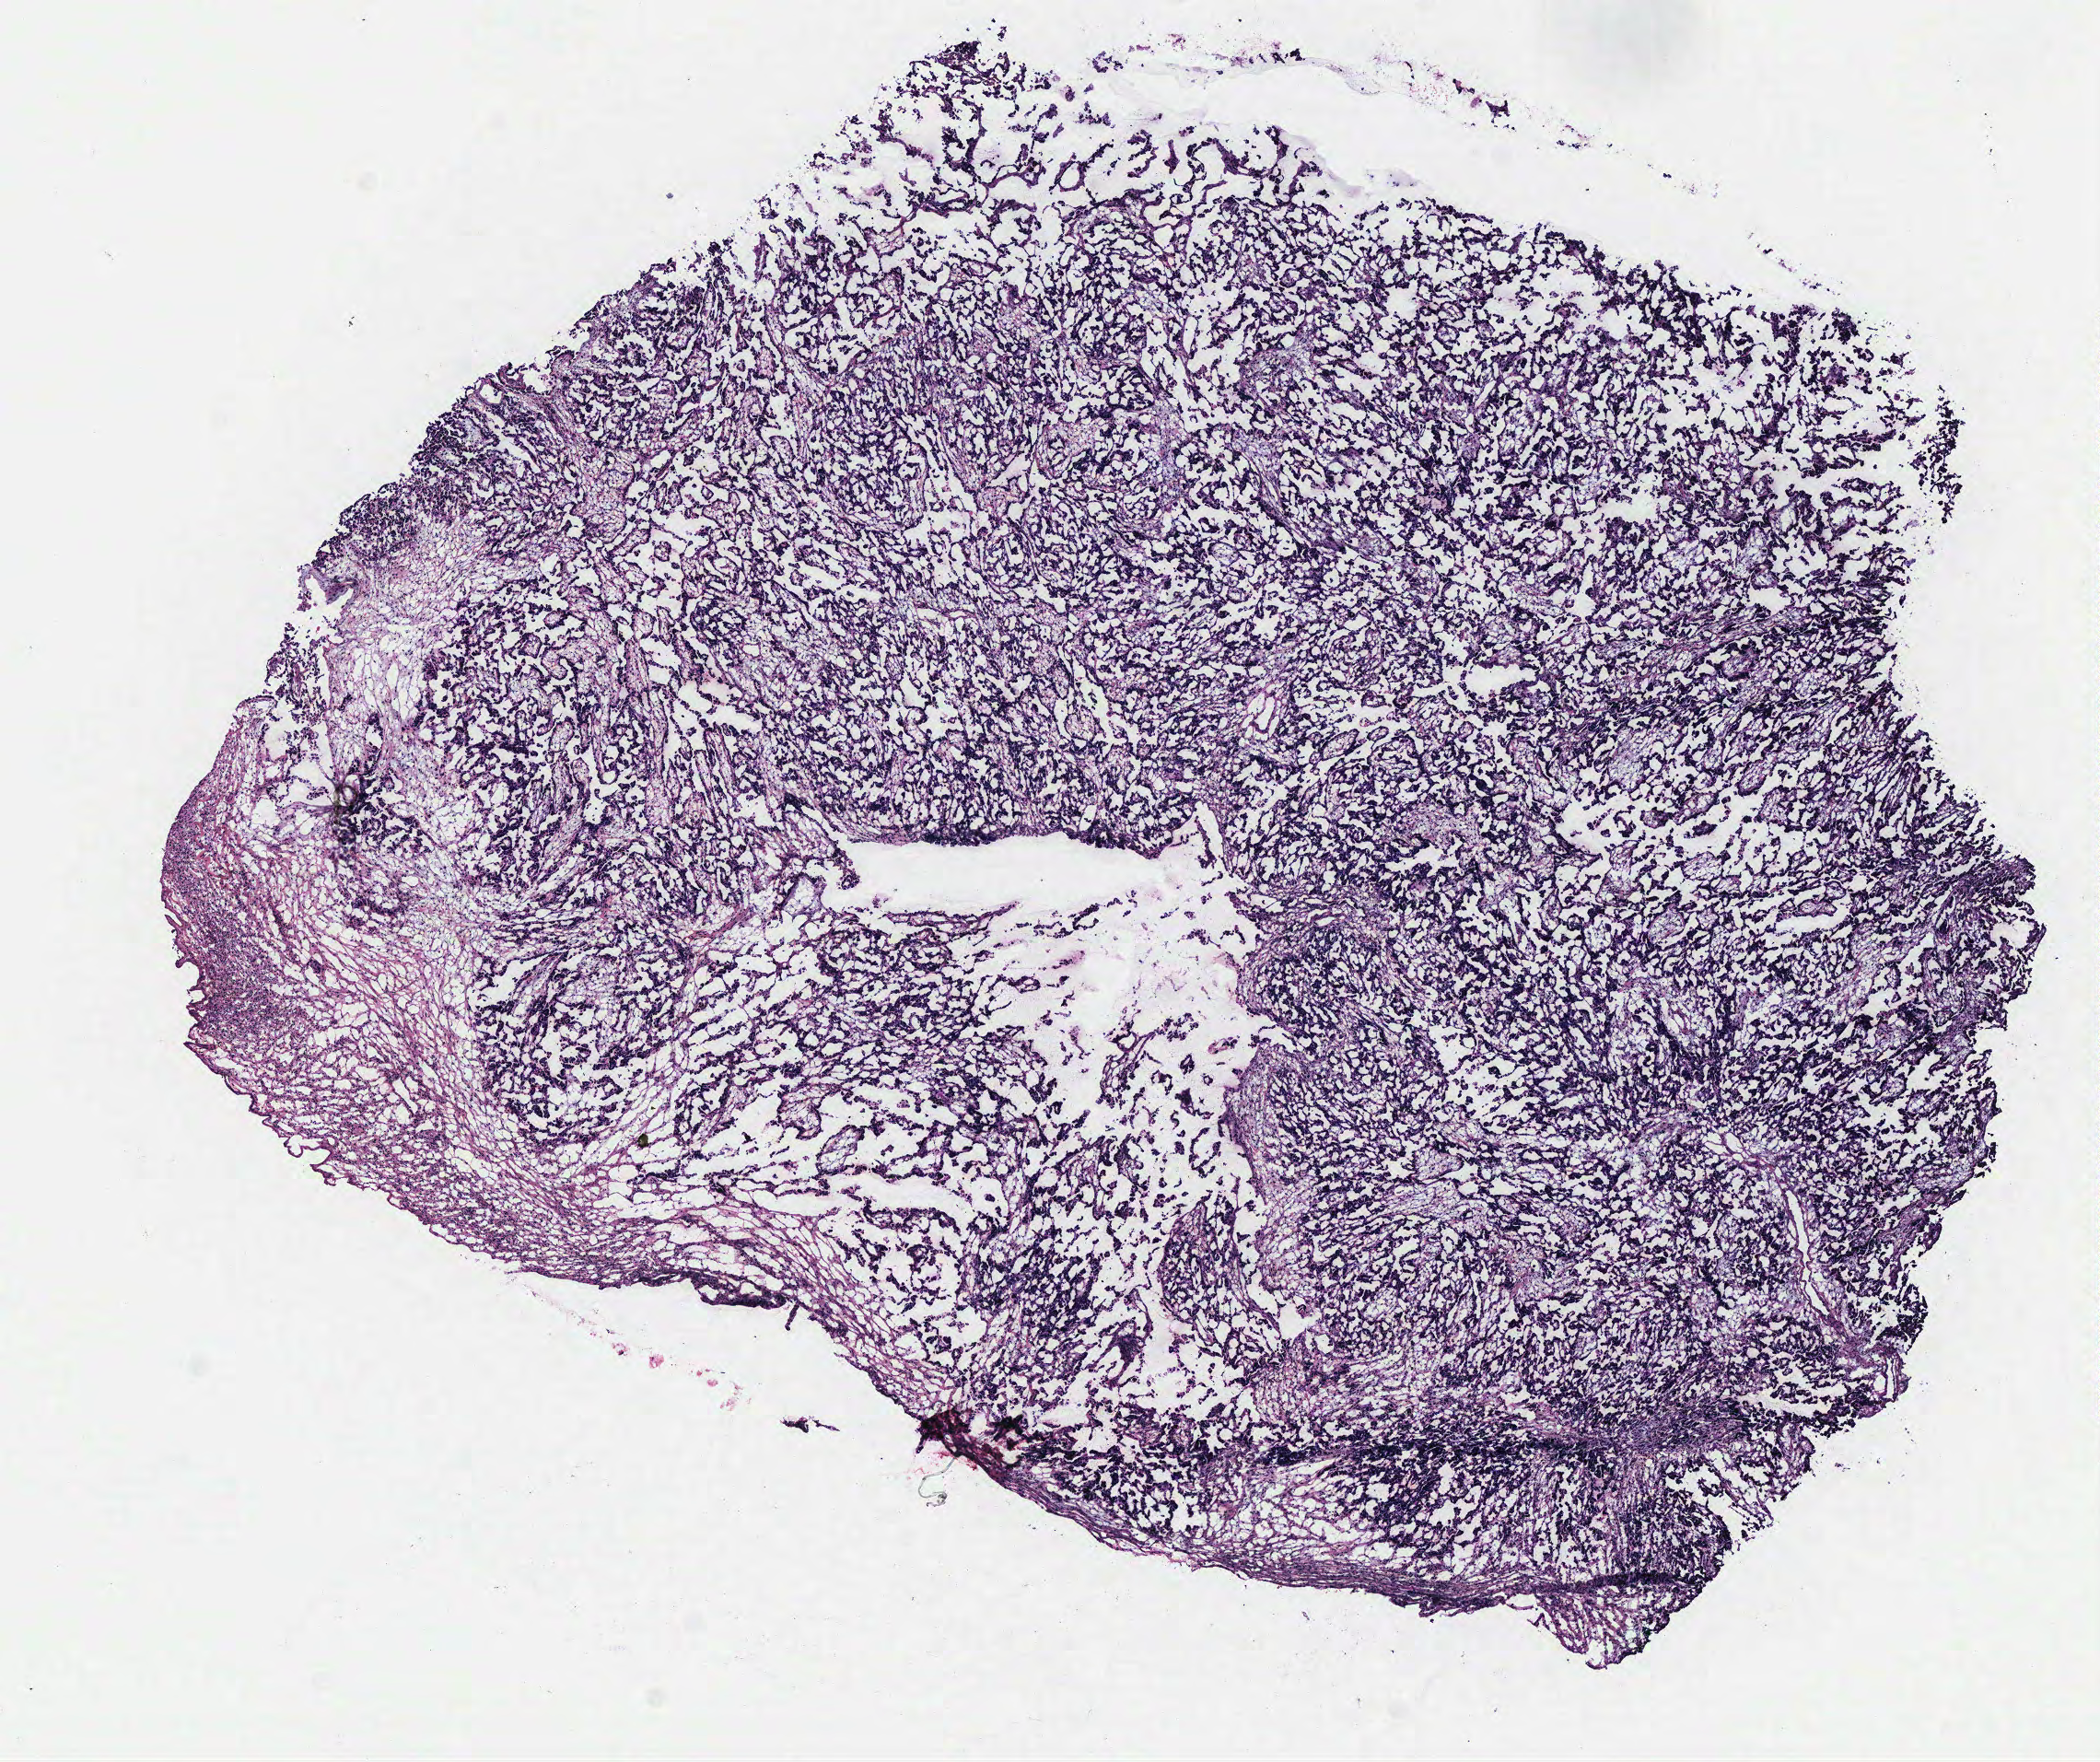
Whole-slide histology image, H&E-stained — whole scanned area (about 9.1 x 7.7 mm, acquisition: 40x scan) shown as a low-resolution overview. Ovary, tumour tissue. Female, 74 y/o.
Diagnosis: Serous adenocarcinoma, NOS. Primary tumour site (as recorded): peritoneum.